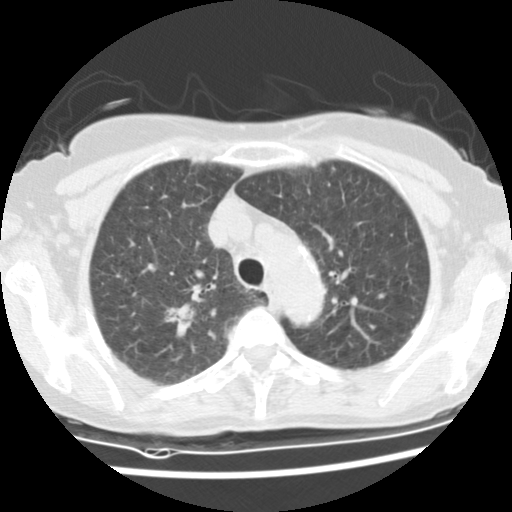
Low-dose screening chest CT, one axial slice; position 106 of 134 along the scan axis; reconstruction kernel STANDARD; lung window (W 1500 / L -600 HU); 2.5 mm slice thickness; 512 × 512 image matrix, field of view 298 × 298 mm.
Structures marked on this image (expert manual segmentation):
- lesion 1 (tumor, upper lobe of right lung): box from (x=164, y=301) to (x=197, y=337) px